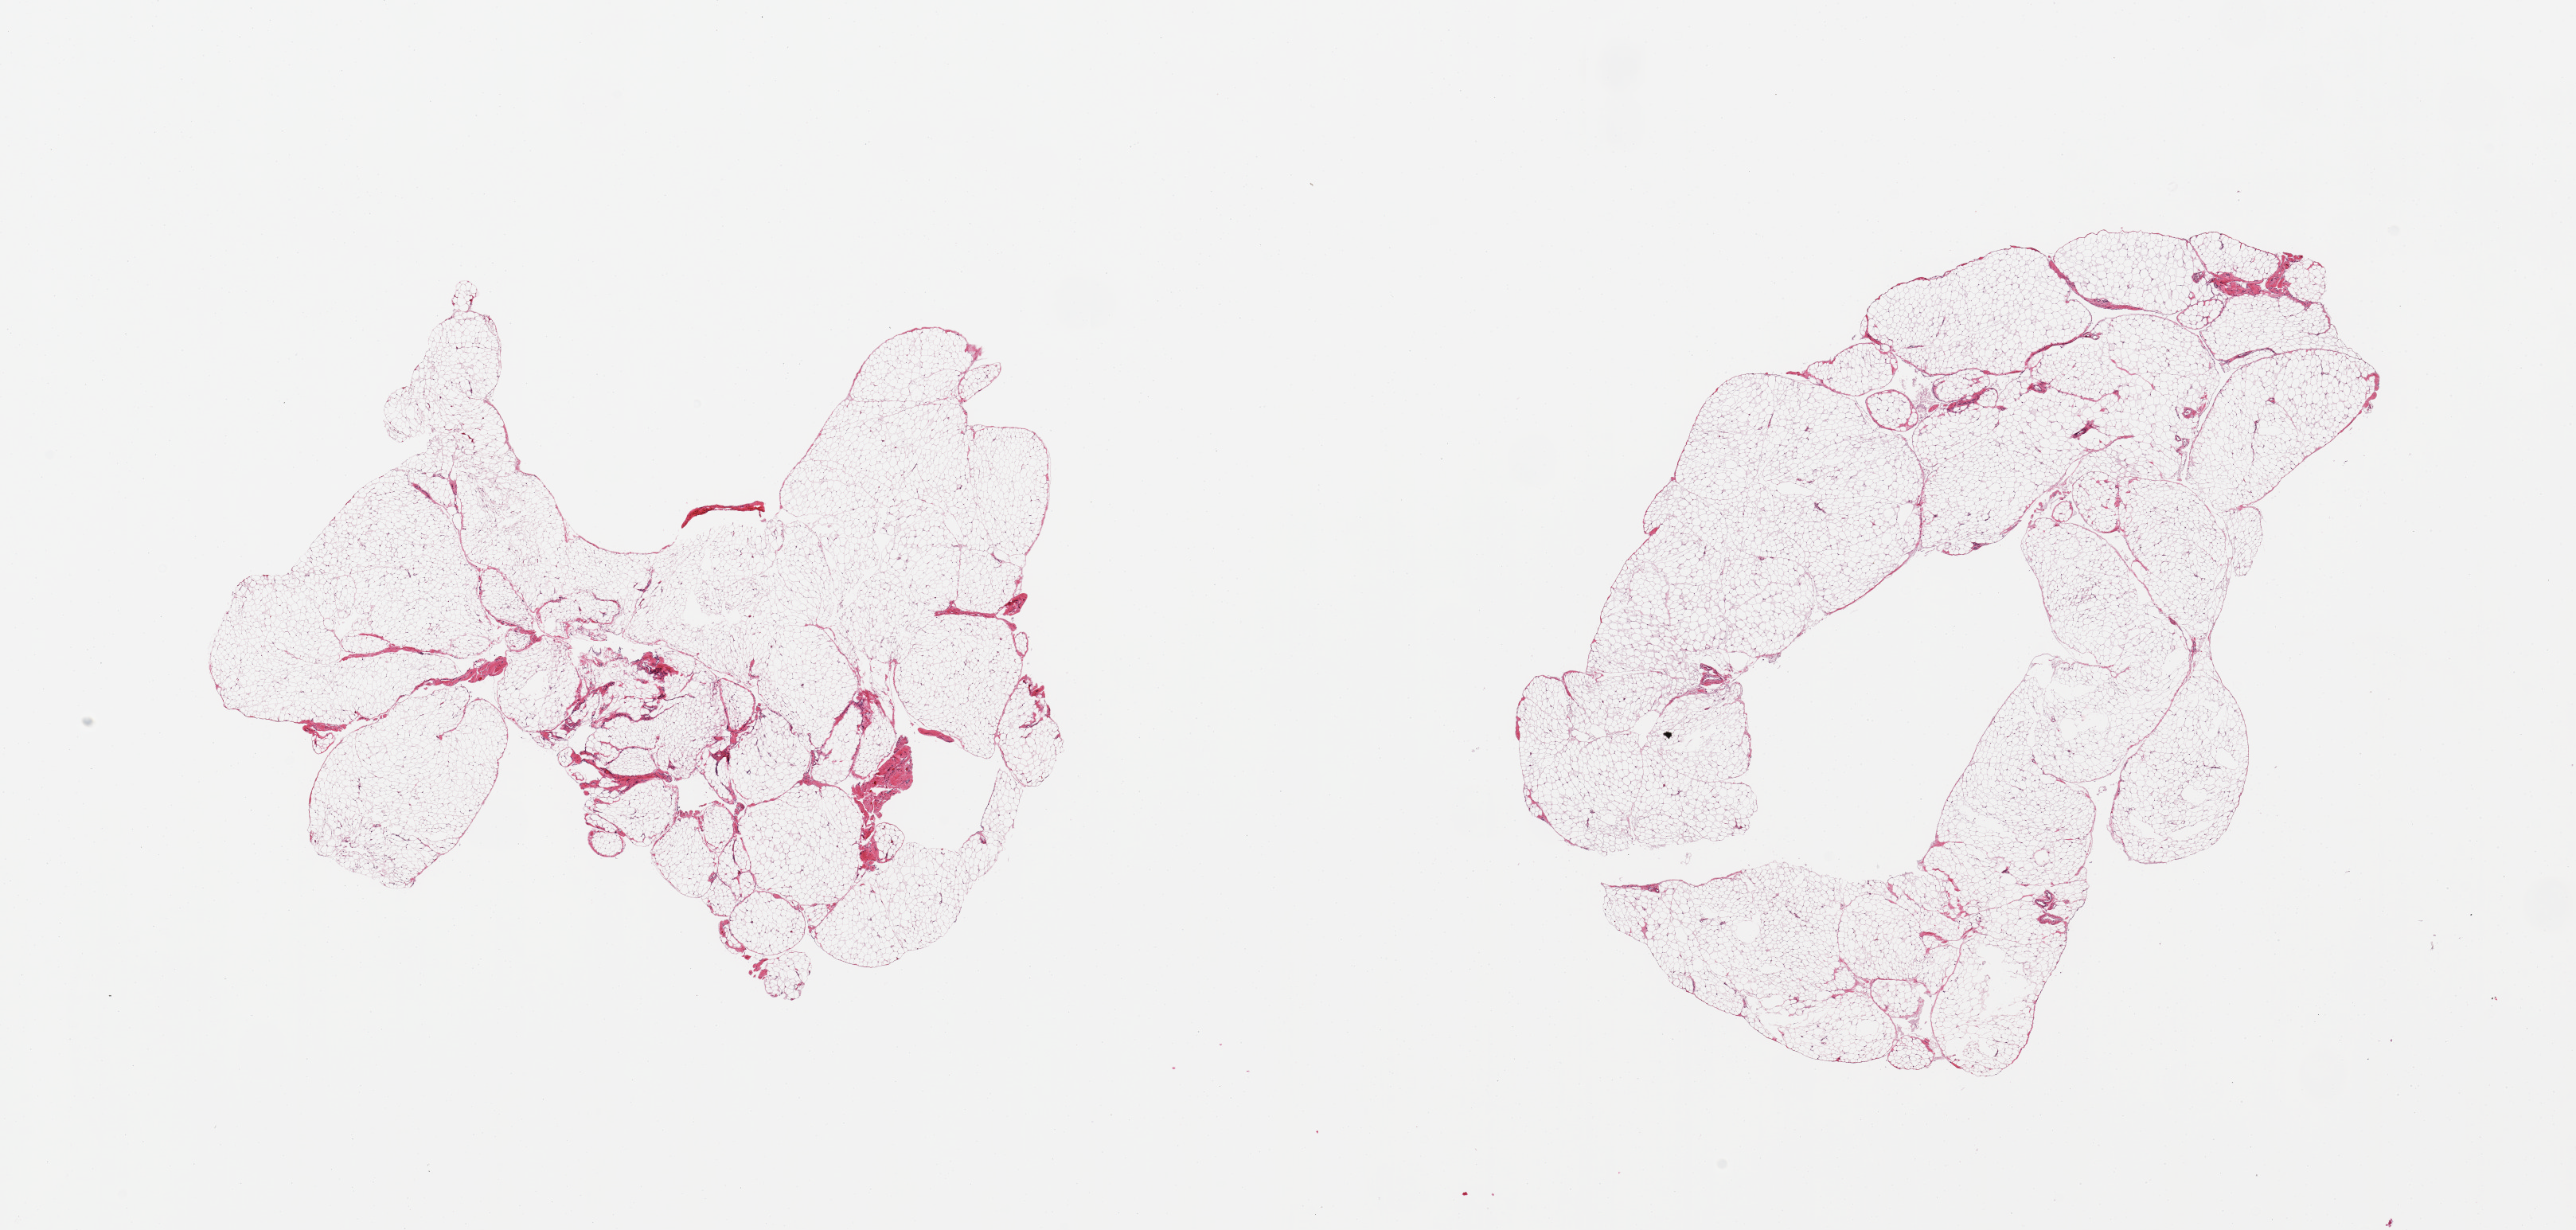
Haematoxylin and eosin whole-slide image, low-resolution overview of the scanned area, about 25.6 x 12.2 mm (from a 20x scan), PAXgene-fixed paraffin-embedded (PFPE) section, sampled site (target tissue): omentum, donor tissue sample. Male donor.
Pathologist's review note for this sample: 2 pieces.